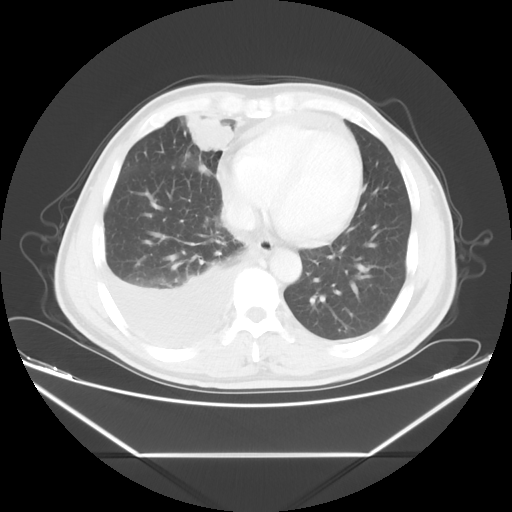
Chest CT, one axial slice; slice 18 of 56 in the series (ordered by position); reconstruction kernel STANDARD; 120 kVp; lung window (W 1500 / L -600 HU); 5 mm slice thickness; 512 × 512 image matrix. Male patient, age 57 years. From the clinical record (not read from this slice): clinical TNM (as recorded): T2 N3 M1.
Annotated regions visible in this slice (bounding box drawn by a radiologist):
- lung tumour (recorded histology: adenocarcinoma): bounding box <181,109,239,159> (left, top, right, bottom; pixels)